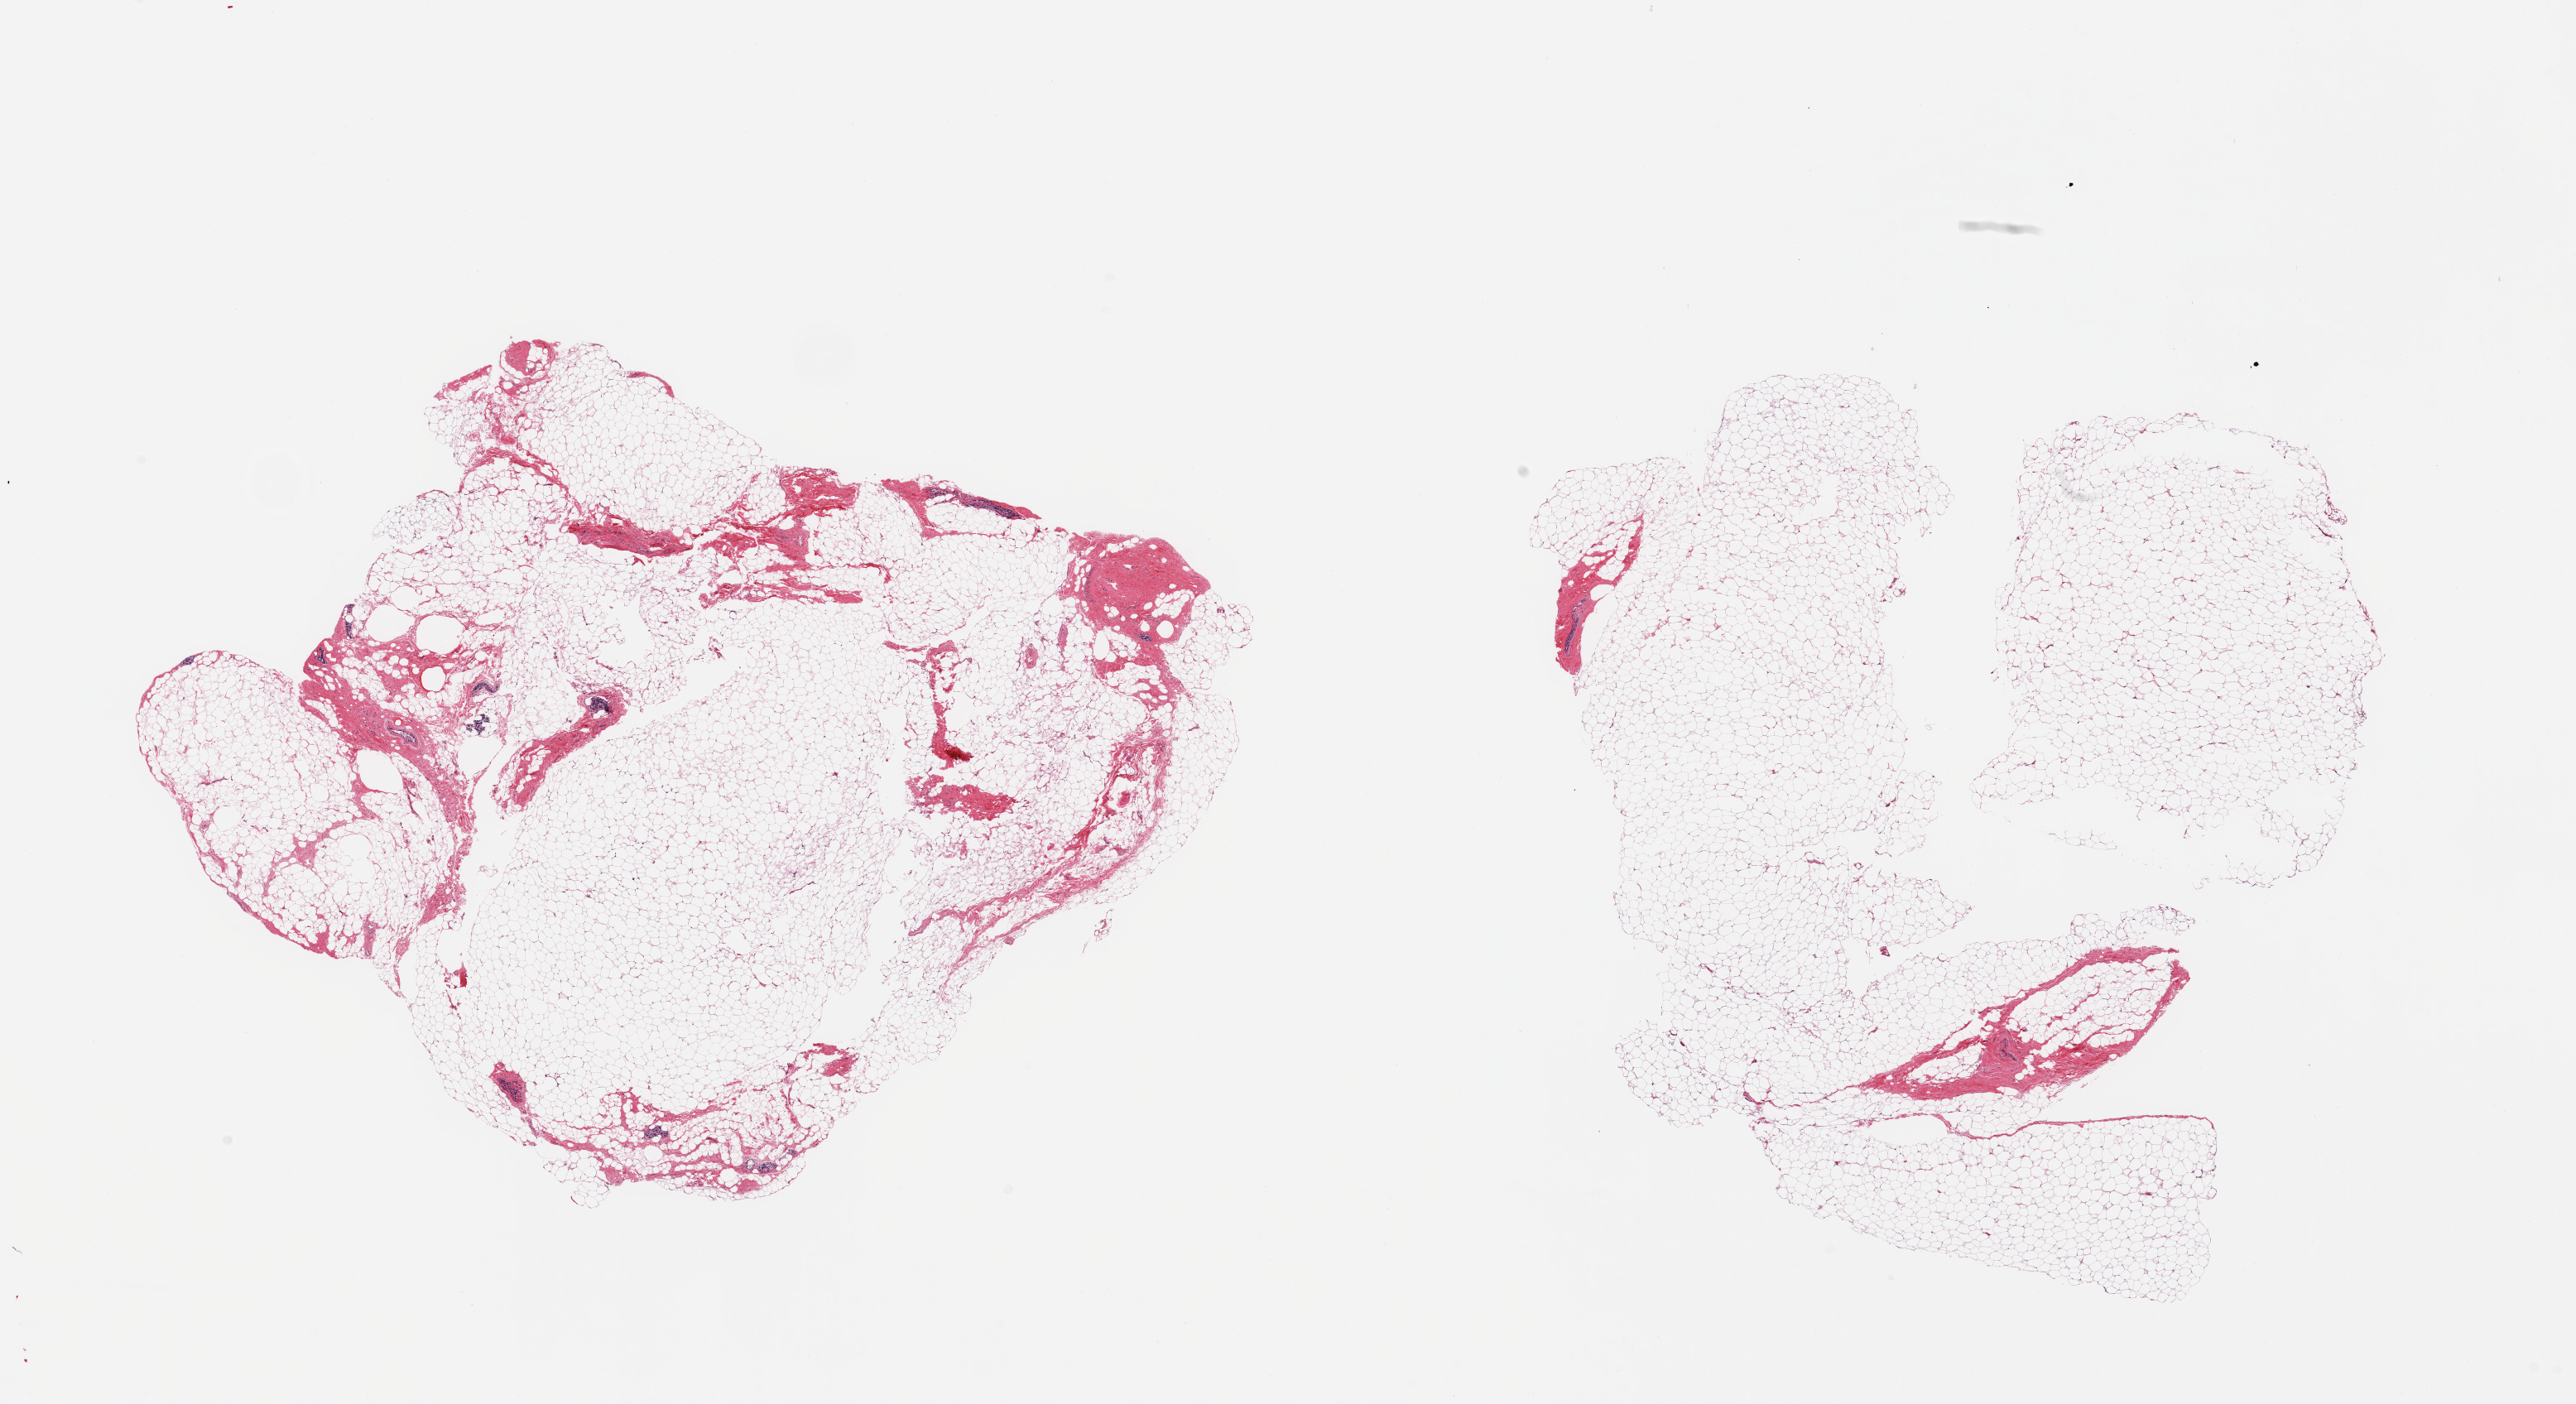
H&E whole-slide image, brightfield — low-resolution overview of the scanned area, about 24.6 x 13.4 mm (slide scanned at 20x). PAXgene-fixed, paraffin-embedded tissue. Sampled site (target tissue): breast. Donor tissue sample. Female donor.
Review note (as recorded): 2 pieces; atrophic >90% fat; scattered small ducts.